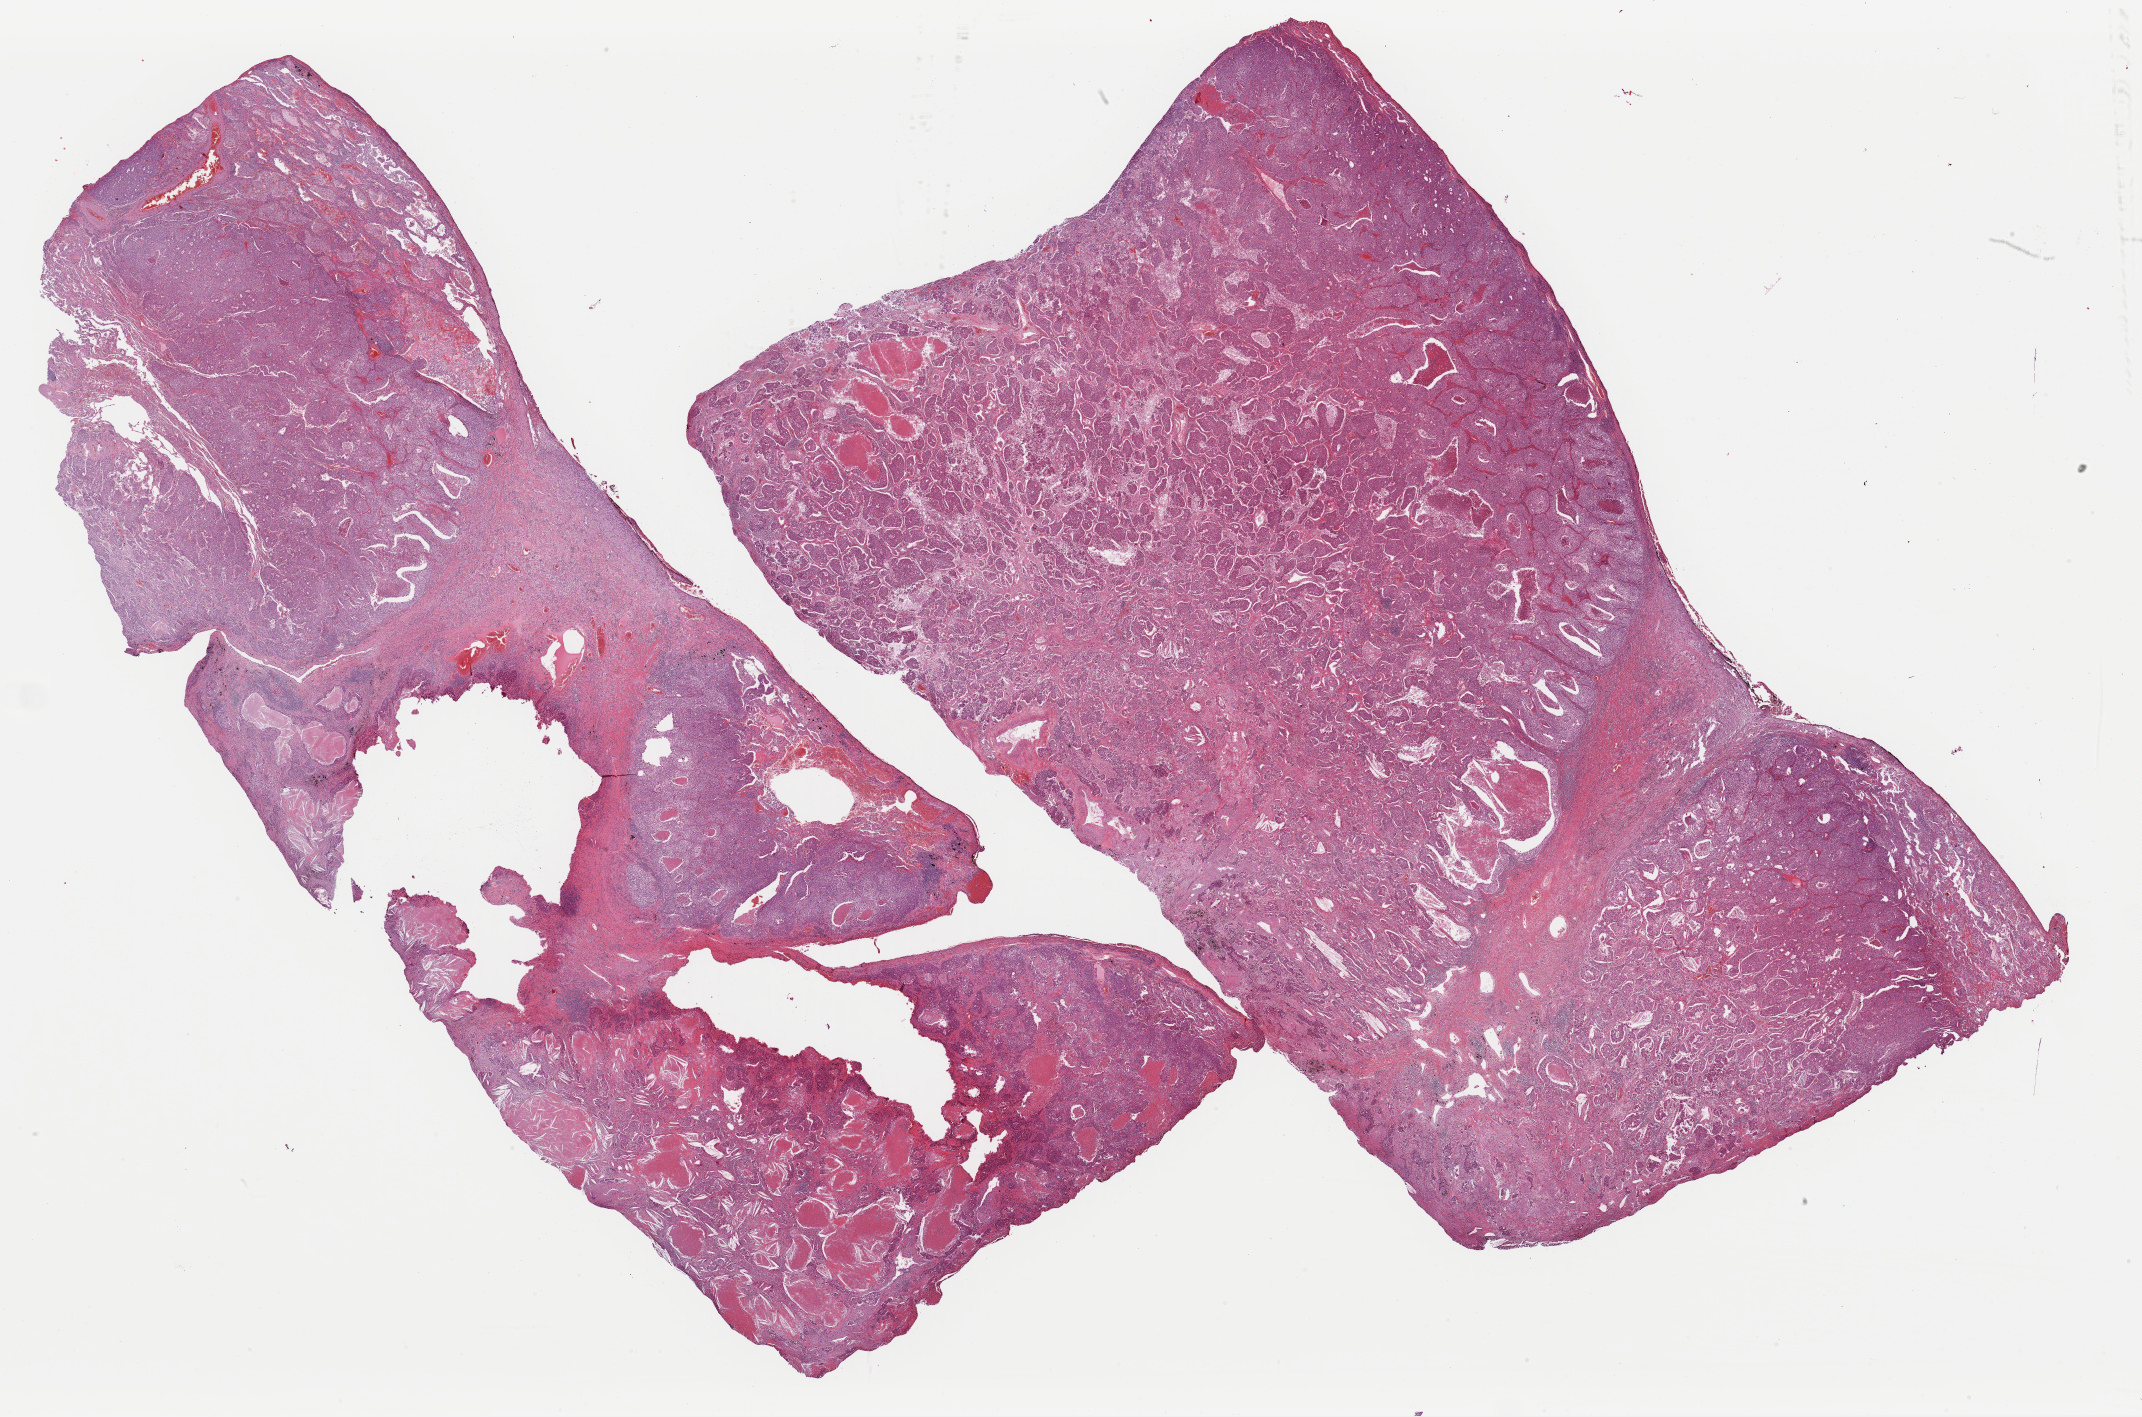
Whole-slide histology image, Hematoxylin and eosin (H&E) stained — low-resolution overview of the scanned area, about 33.8 x 22.4 mm. FFPE section. Sample: primary tumour, lung. Male, age 63 years at initial diagnosis.
Pathologic diagnosis: Acinar cell carcinoma (upper lobe, lung).